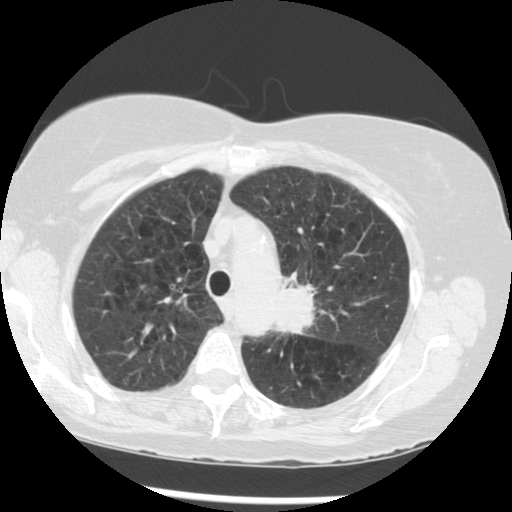
Axial slice from a low-dose chest CT screening exam; third annual screen; lung window (W 1500 / L -600 HU); 512 × 512 image matrix, field of view 330 × 330 mm. Female, age 70 years at enrolment.
- Expert-annotated lung lesion, bounding box (x1, y1, x2, y2) in pixels: (266, 267, 360, 357).
- The exam's reader record, not a measurement of the box and not confirmed to be the same lesion: non-calcified nodule or mass ≥4 mm, left upper lobe, 32 × 26 mm, spiculated (stellate) margins, soft tissue attenuation, pre-existing on the prior screen: yes; interval growth: yes.
- Official screen result: positive, other.
- Participant outcome: lung cancer diagnosed 24 days after this screen — neoplasm, malignant, left upper lobe, stage IIIB (AJCC 6th edition), 40 mm at pathology.